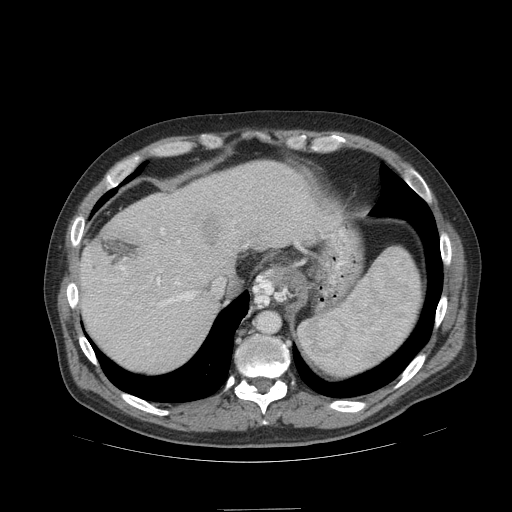
Contrast-enhanced abdominal CT (liver protocol), one axial slice. Position 82 of 99 along the scan axis. Reconstruction kernel STANDARD. 140 kVp. Soft-tissue window (W 400 / L 40 HU). 2.5 mm slice thickness. 512 × 512 image matrix. Case-level facts recorded for this patient, not image findings: diagnosis: hepatocellular carcinoma (patient treated with transarterial chemoembolisation; whether this scan precedes or follows treatment is not stated here); TNM stage (as recorded): Stage-I; Child-Pugh class: A; tumour differentiation: no biopsy; tumour nodularity: uninodular.
Structures marked on this image (semi-automatic segmentation, software-assisted and operator-edited):
- liver parenchyma outside the tumour (the mass and vessels are separate outlines, so this box may not span the whole liver): bounding box [x1, y1, x2, y2] px = [80, 160, 340, 372]
- mass: [200, 213, 223, 245]
- liver vessels: [114, 228, 196, 345]